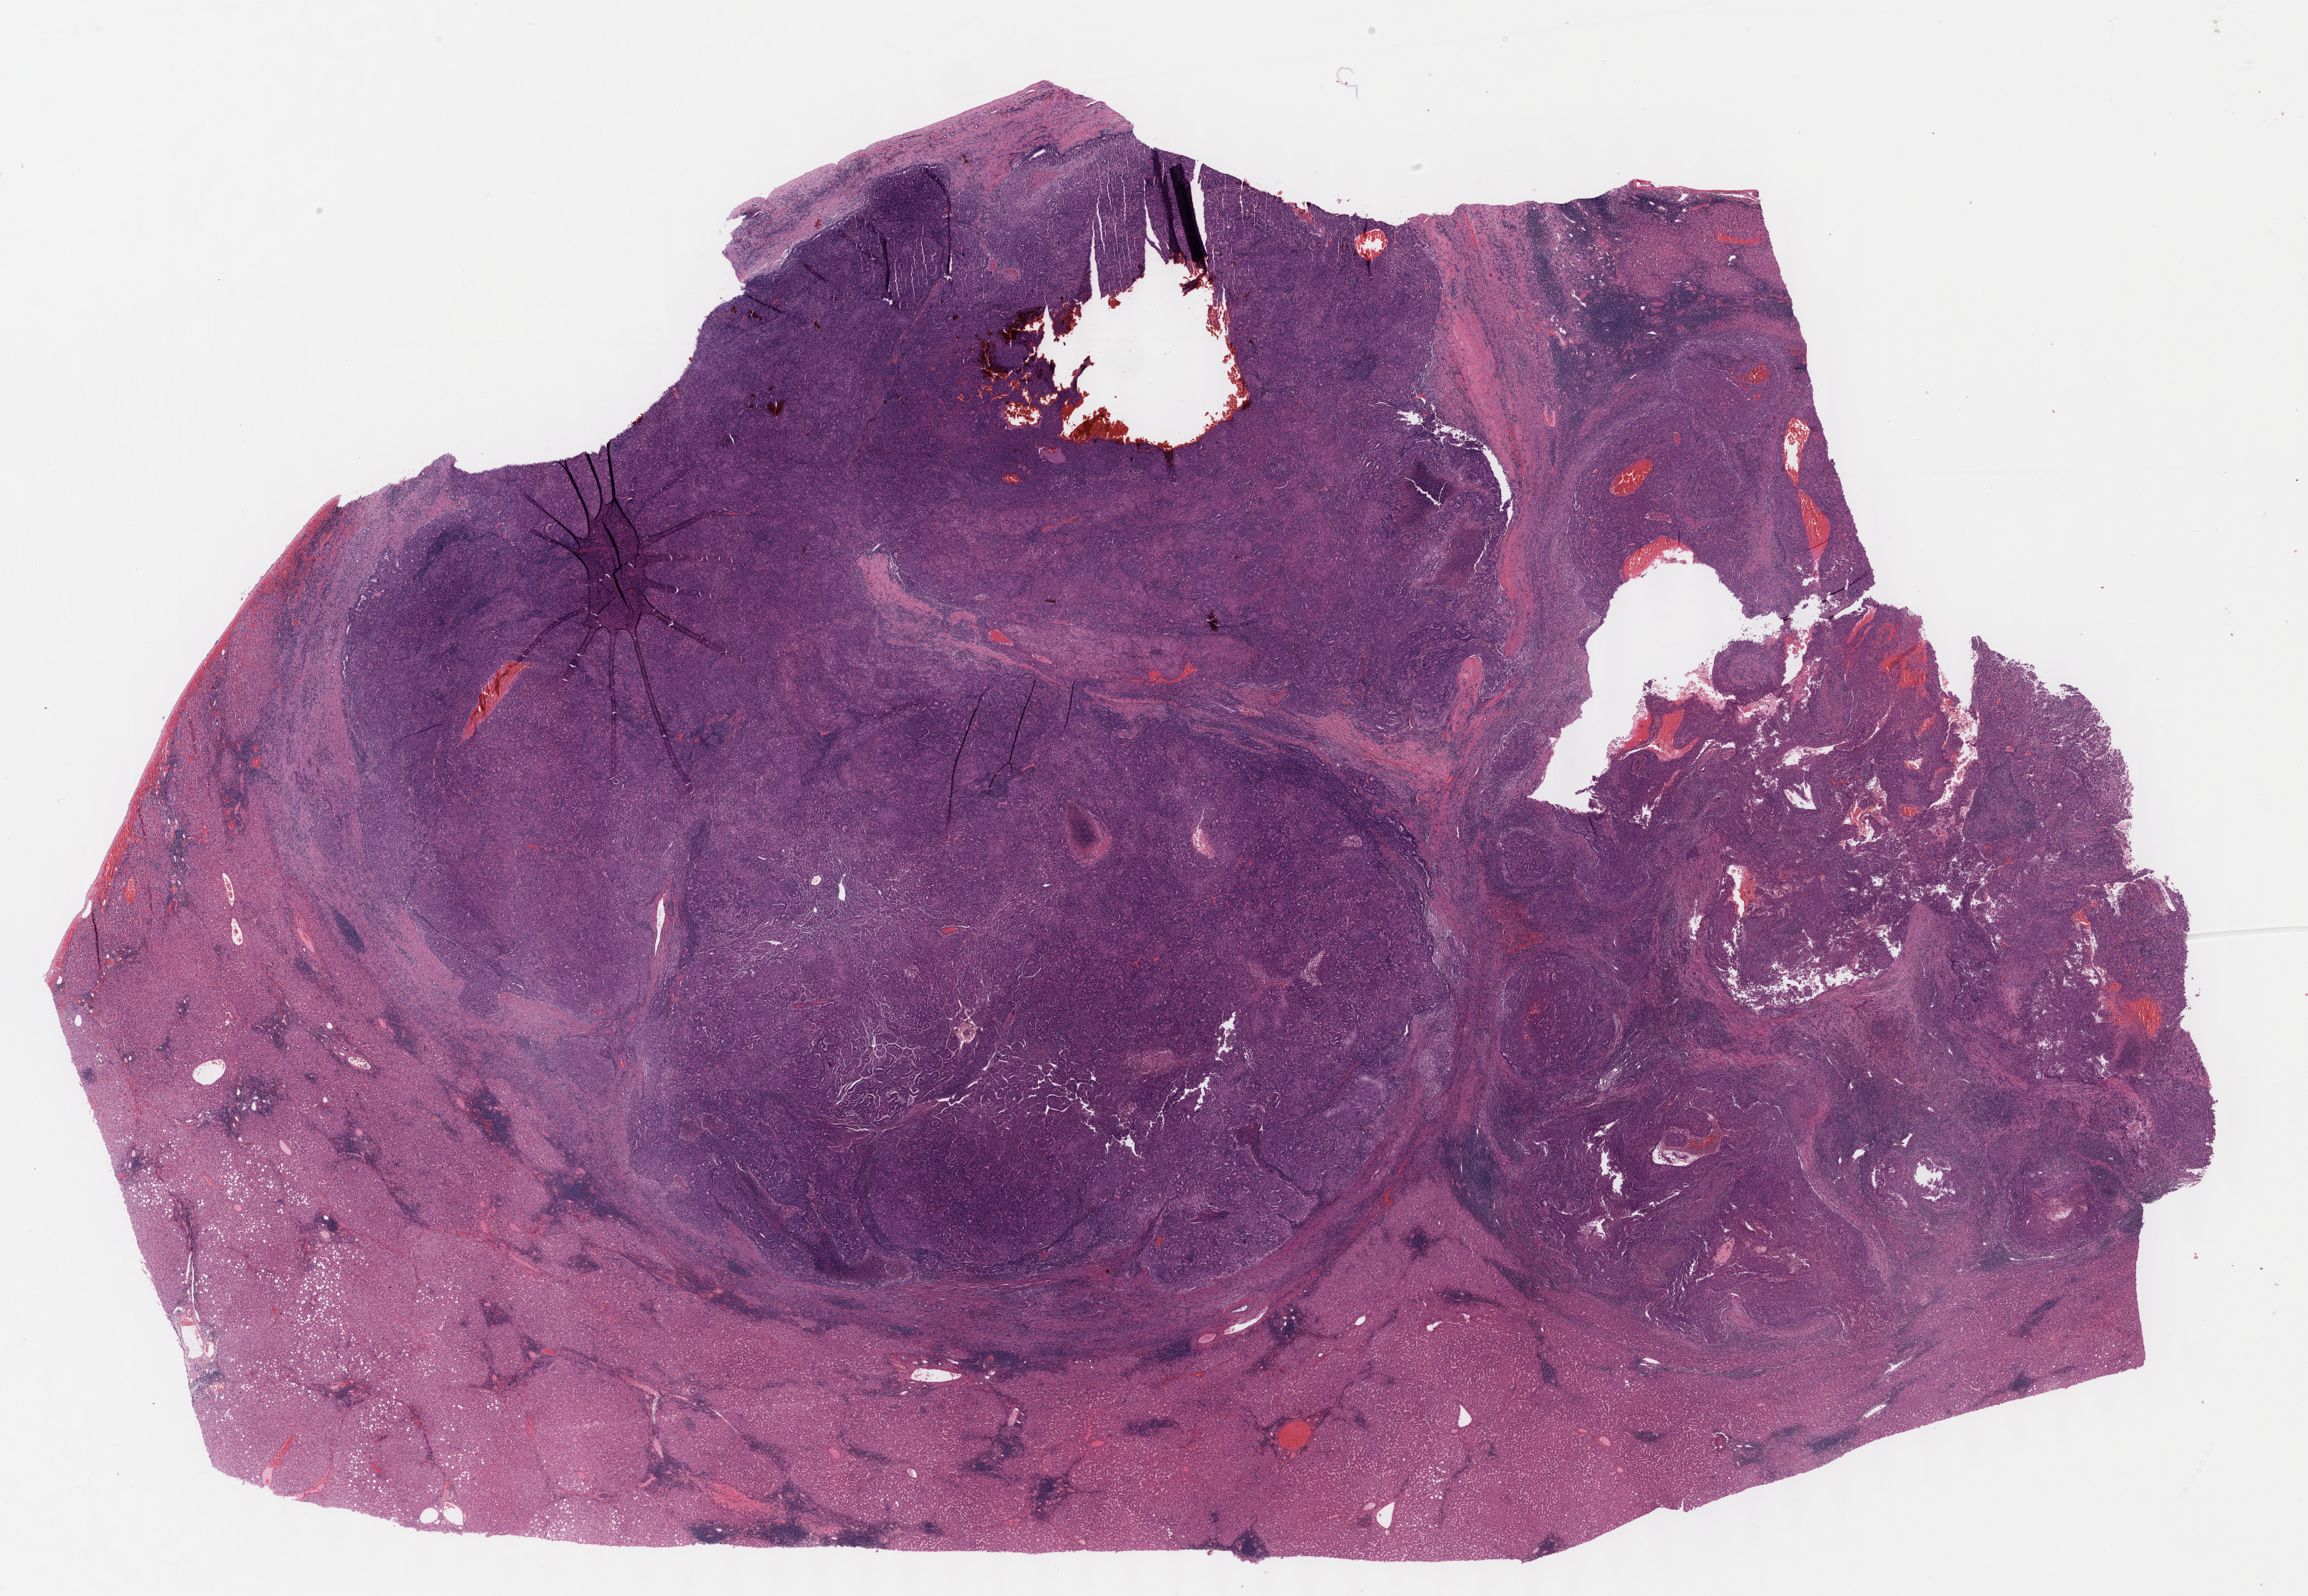
Whole-slide histology image, H&E, shown as a low-resolution overview of the whole scanned area (about 26.2 x 18.1 mm, acquisition: 40x scan), formalin-fixed paraffin-embedded (FFPE) diagnostic section, sample: primary tumour, liver. Male patient; age at initial diagnosis 59 years. Histologic grade: G2 (moderately differentiated).
AJCC pathologic stage: I (7th edition). Diagnosis: Hepatocellular carcinoma, NOS. TNM: T1 NX M0.